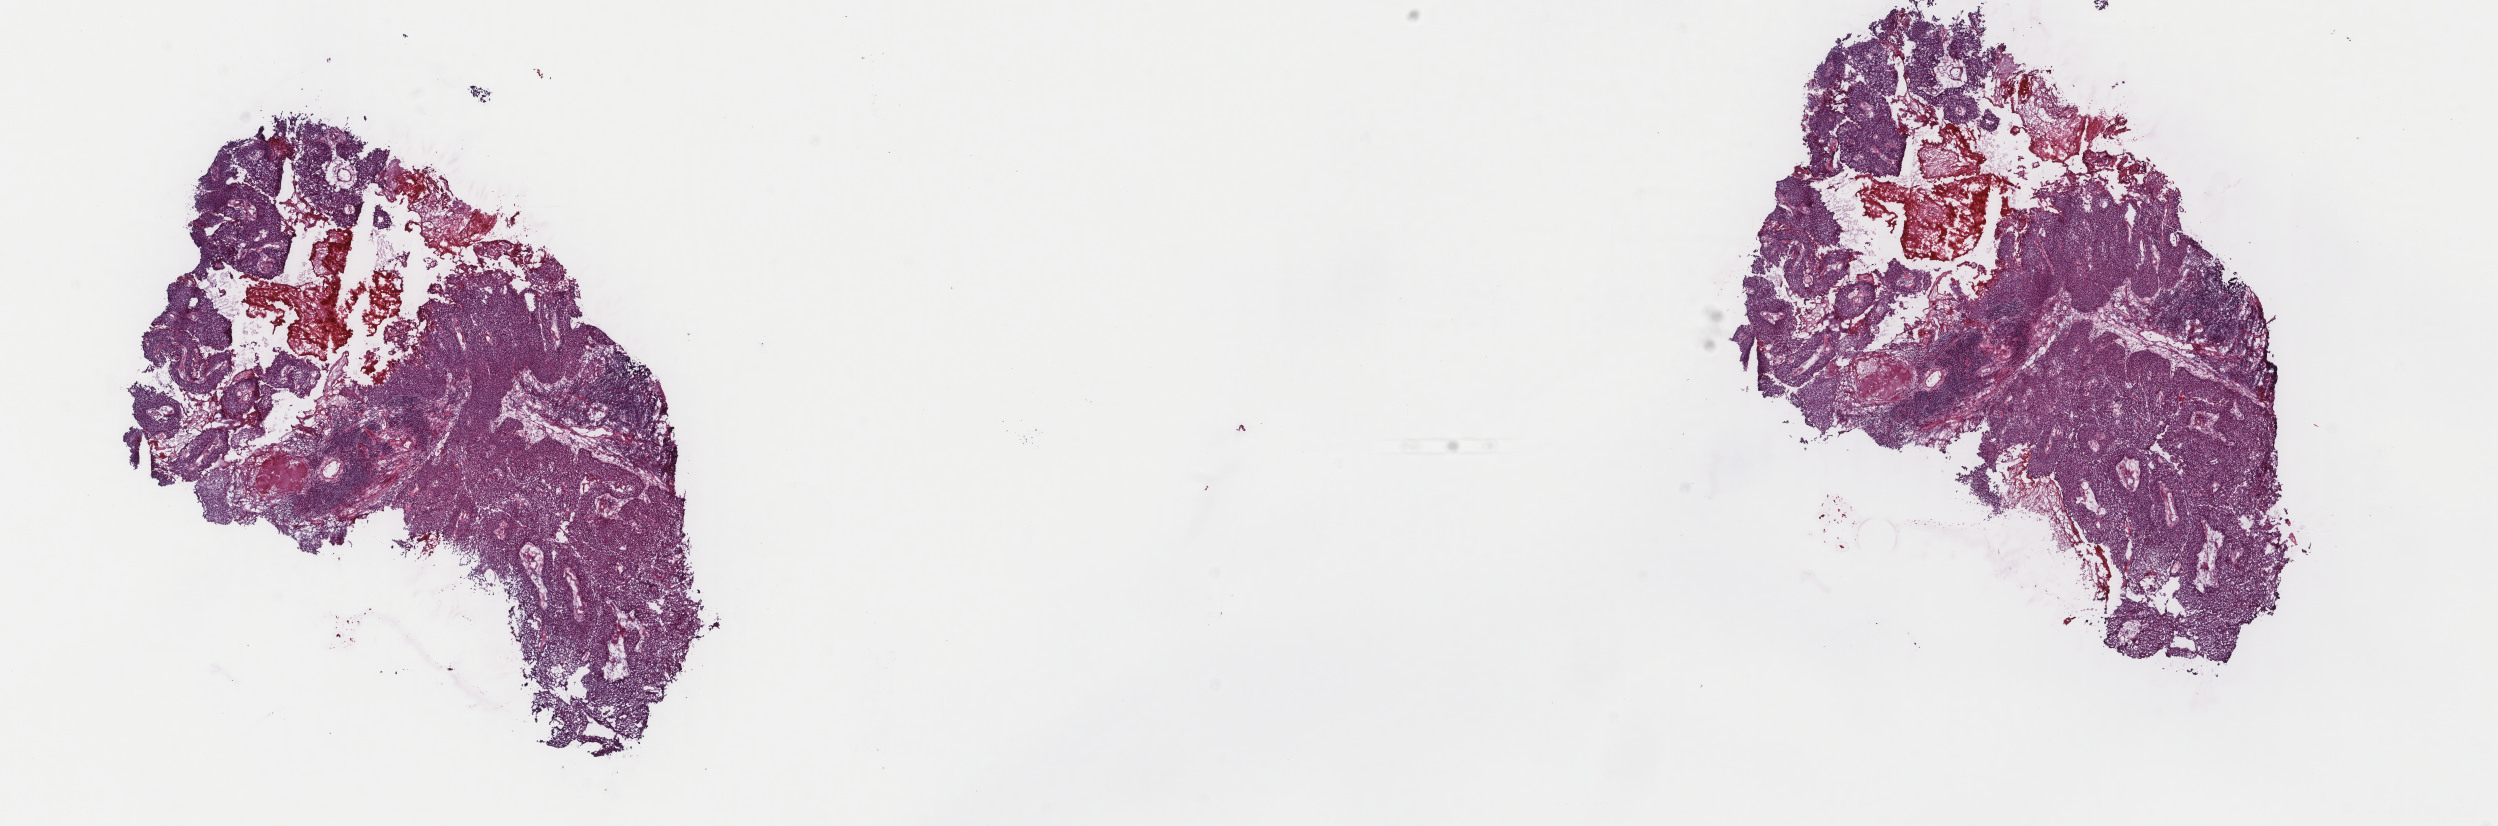
Digitized H&E tissue section (whole slide), a low-resolution overview of the entire scanned area, about 19.8 x 6.6 mm; frozen section; cervix, primary tumour sample. Female patient; age at initial diagnosis 63 years. Composition of this section per pathologist review: tumour cells 80%, tumour nuclei 70%.
Histologic diagnosis: Squamous cell carcinoma, NOS (cervix uteri).